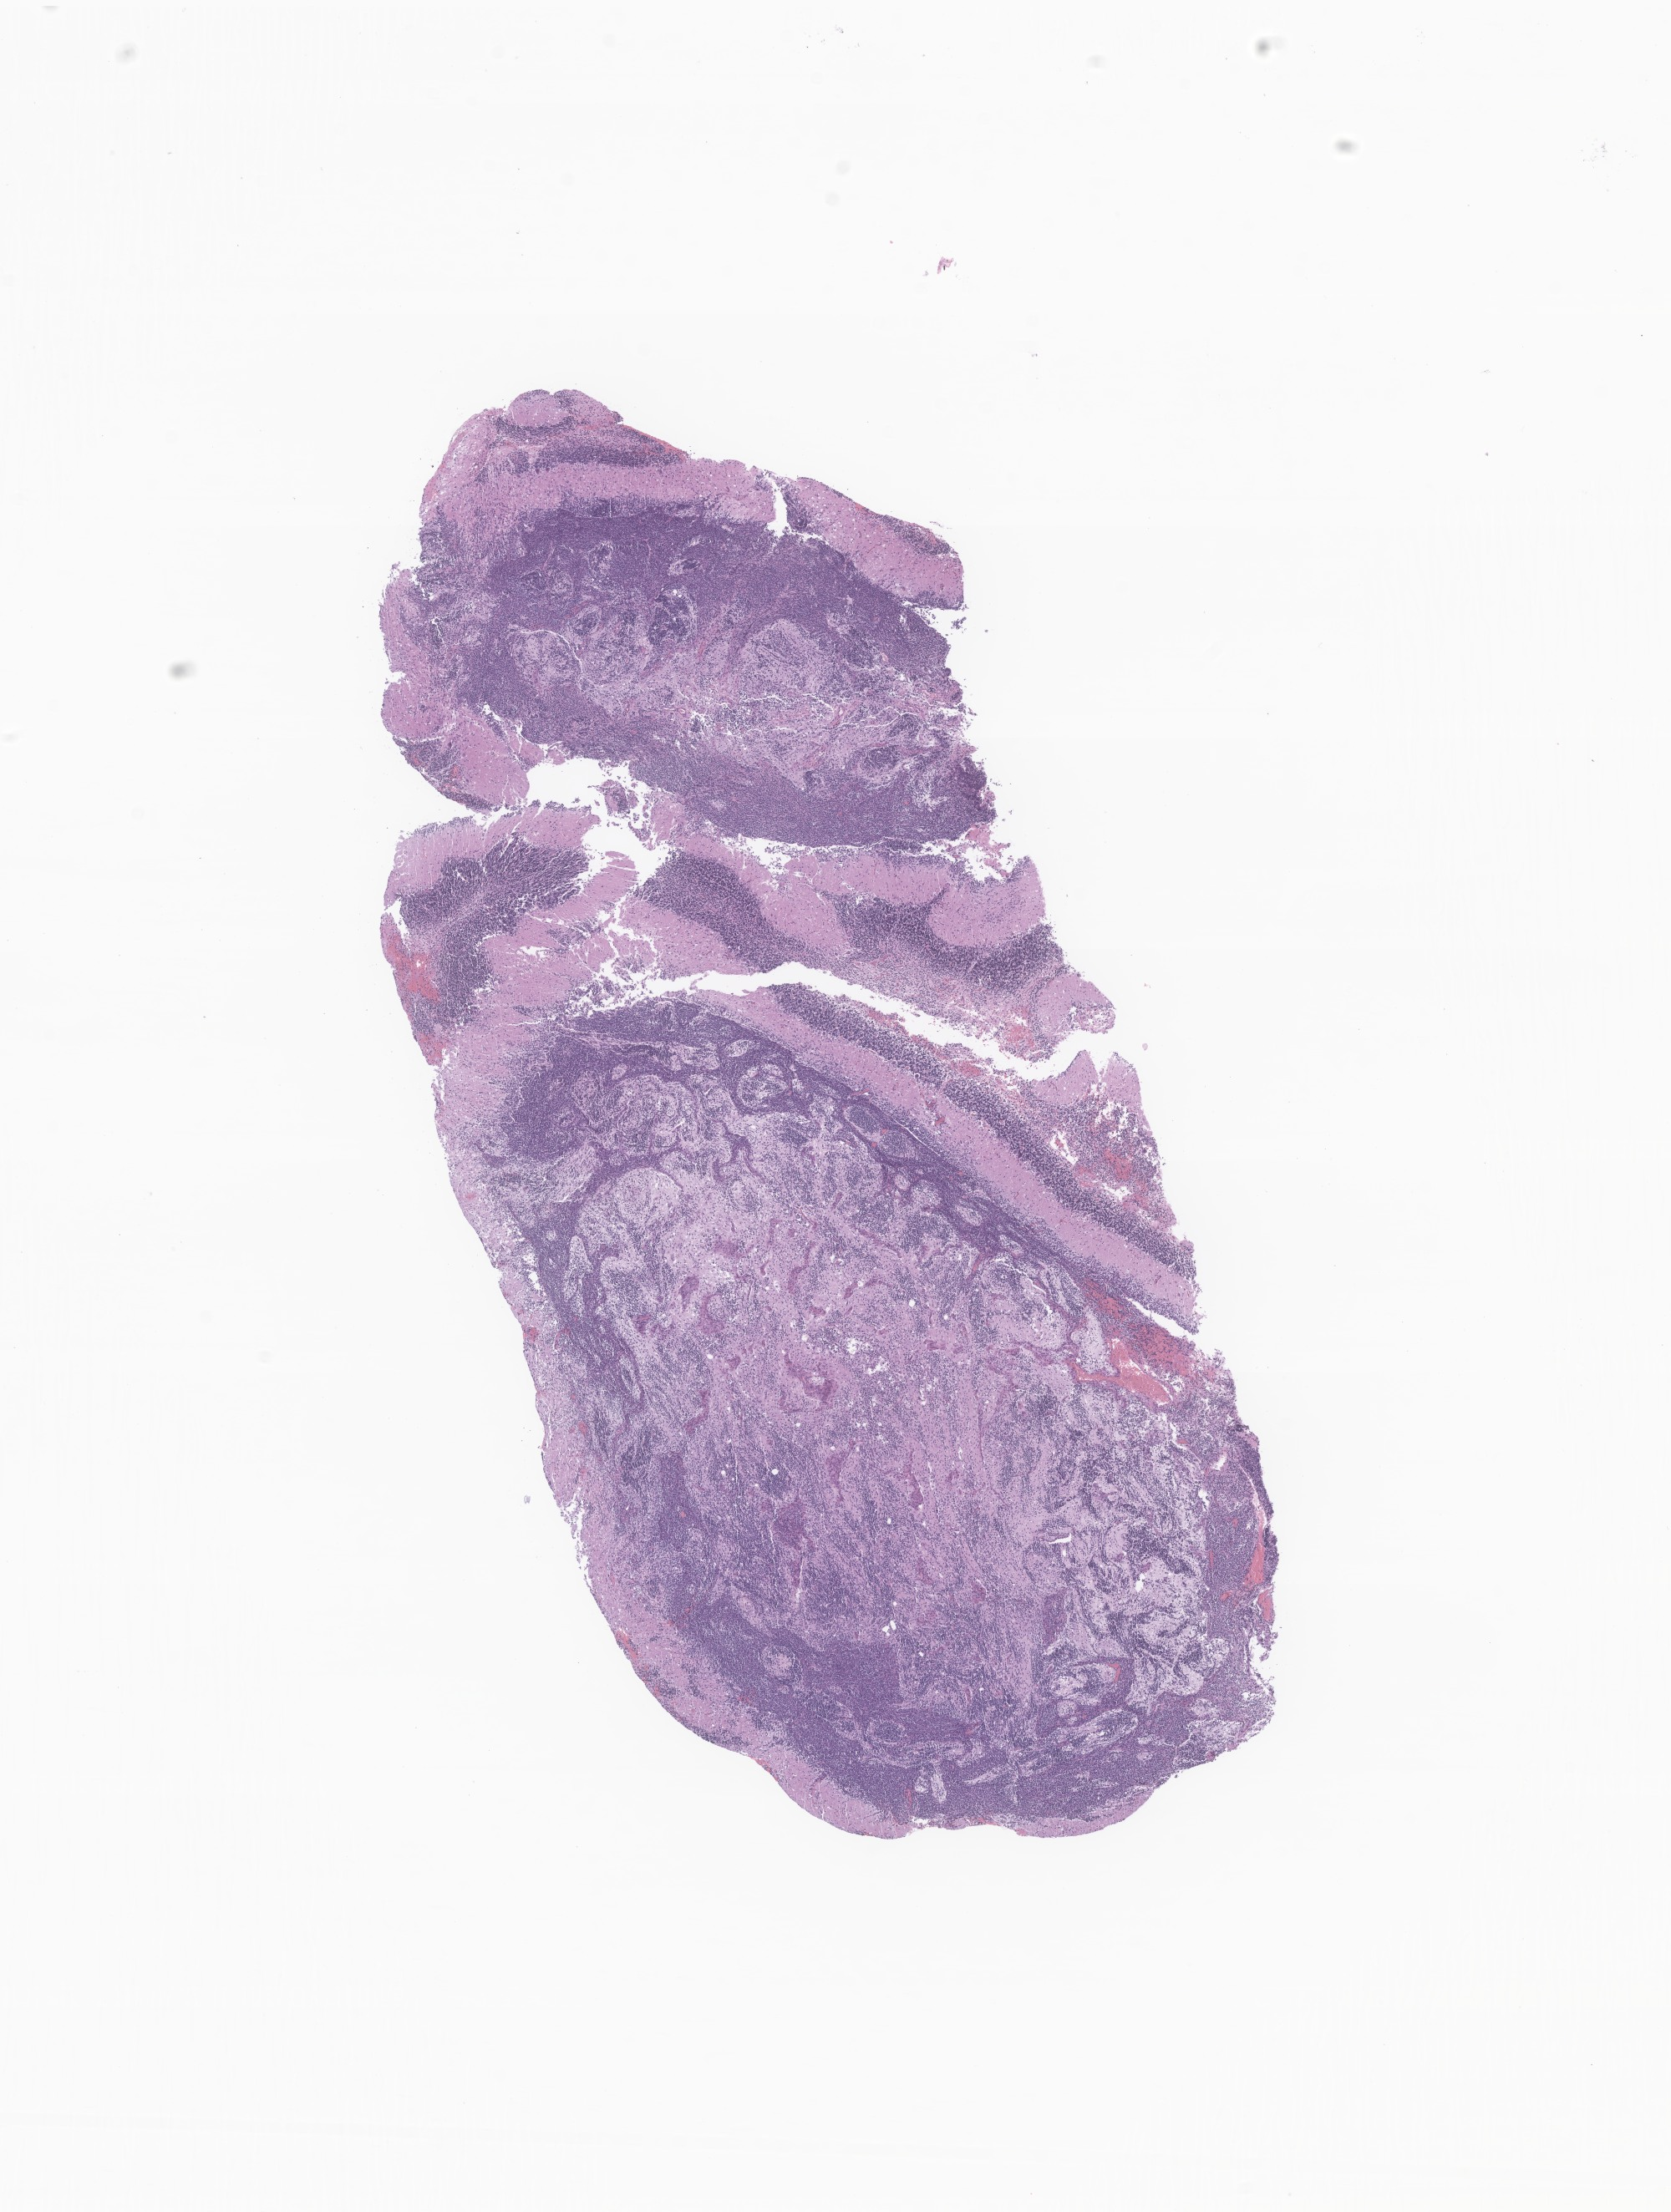
Whole-slide image, haematoxylin and eosin stain of tumor tissue from the brain, shown as a low-resolution overview of the whole scanned area (about 8.4 x 11.2 mm), FFPE section. Patient male; age 180 days.
Diagnosis: Neoplasm, uncertain whether benign or malignant.